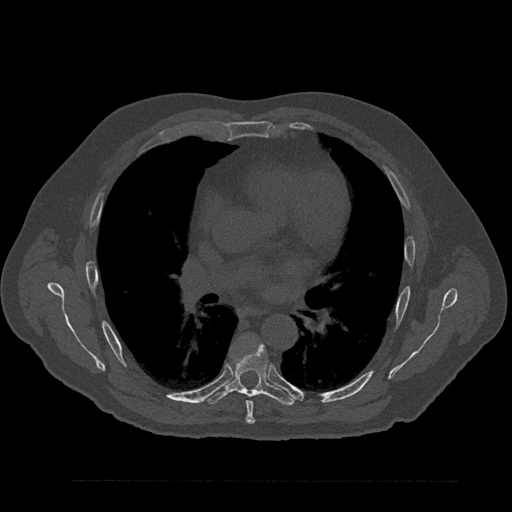
CT including the spine, one axial slice. Slice 525 of 797 in the series (ordered by position). Reconstruction kernel Br40s/3. 120 kVp. Bone window (W 1800 / L 400 HU). 0.5 mm slice thickness. 512 × 512 image matrix, field of view 430 × 430 mm. Patient: male, 61 years. From the clinical record (not read from this slice): primary cancer: prostate.
Outlined on this slice (semi-automatically segmented with operator editing):
- T6 vertebra: bounding box <245,401,255,424> (left, top, right, bottom; pixels)
- T7 vertebra: <204,341,295,406>